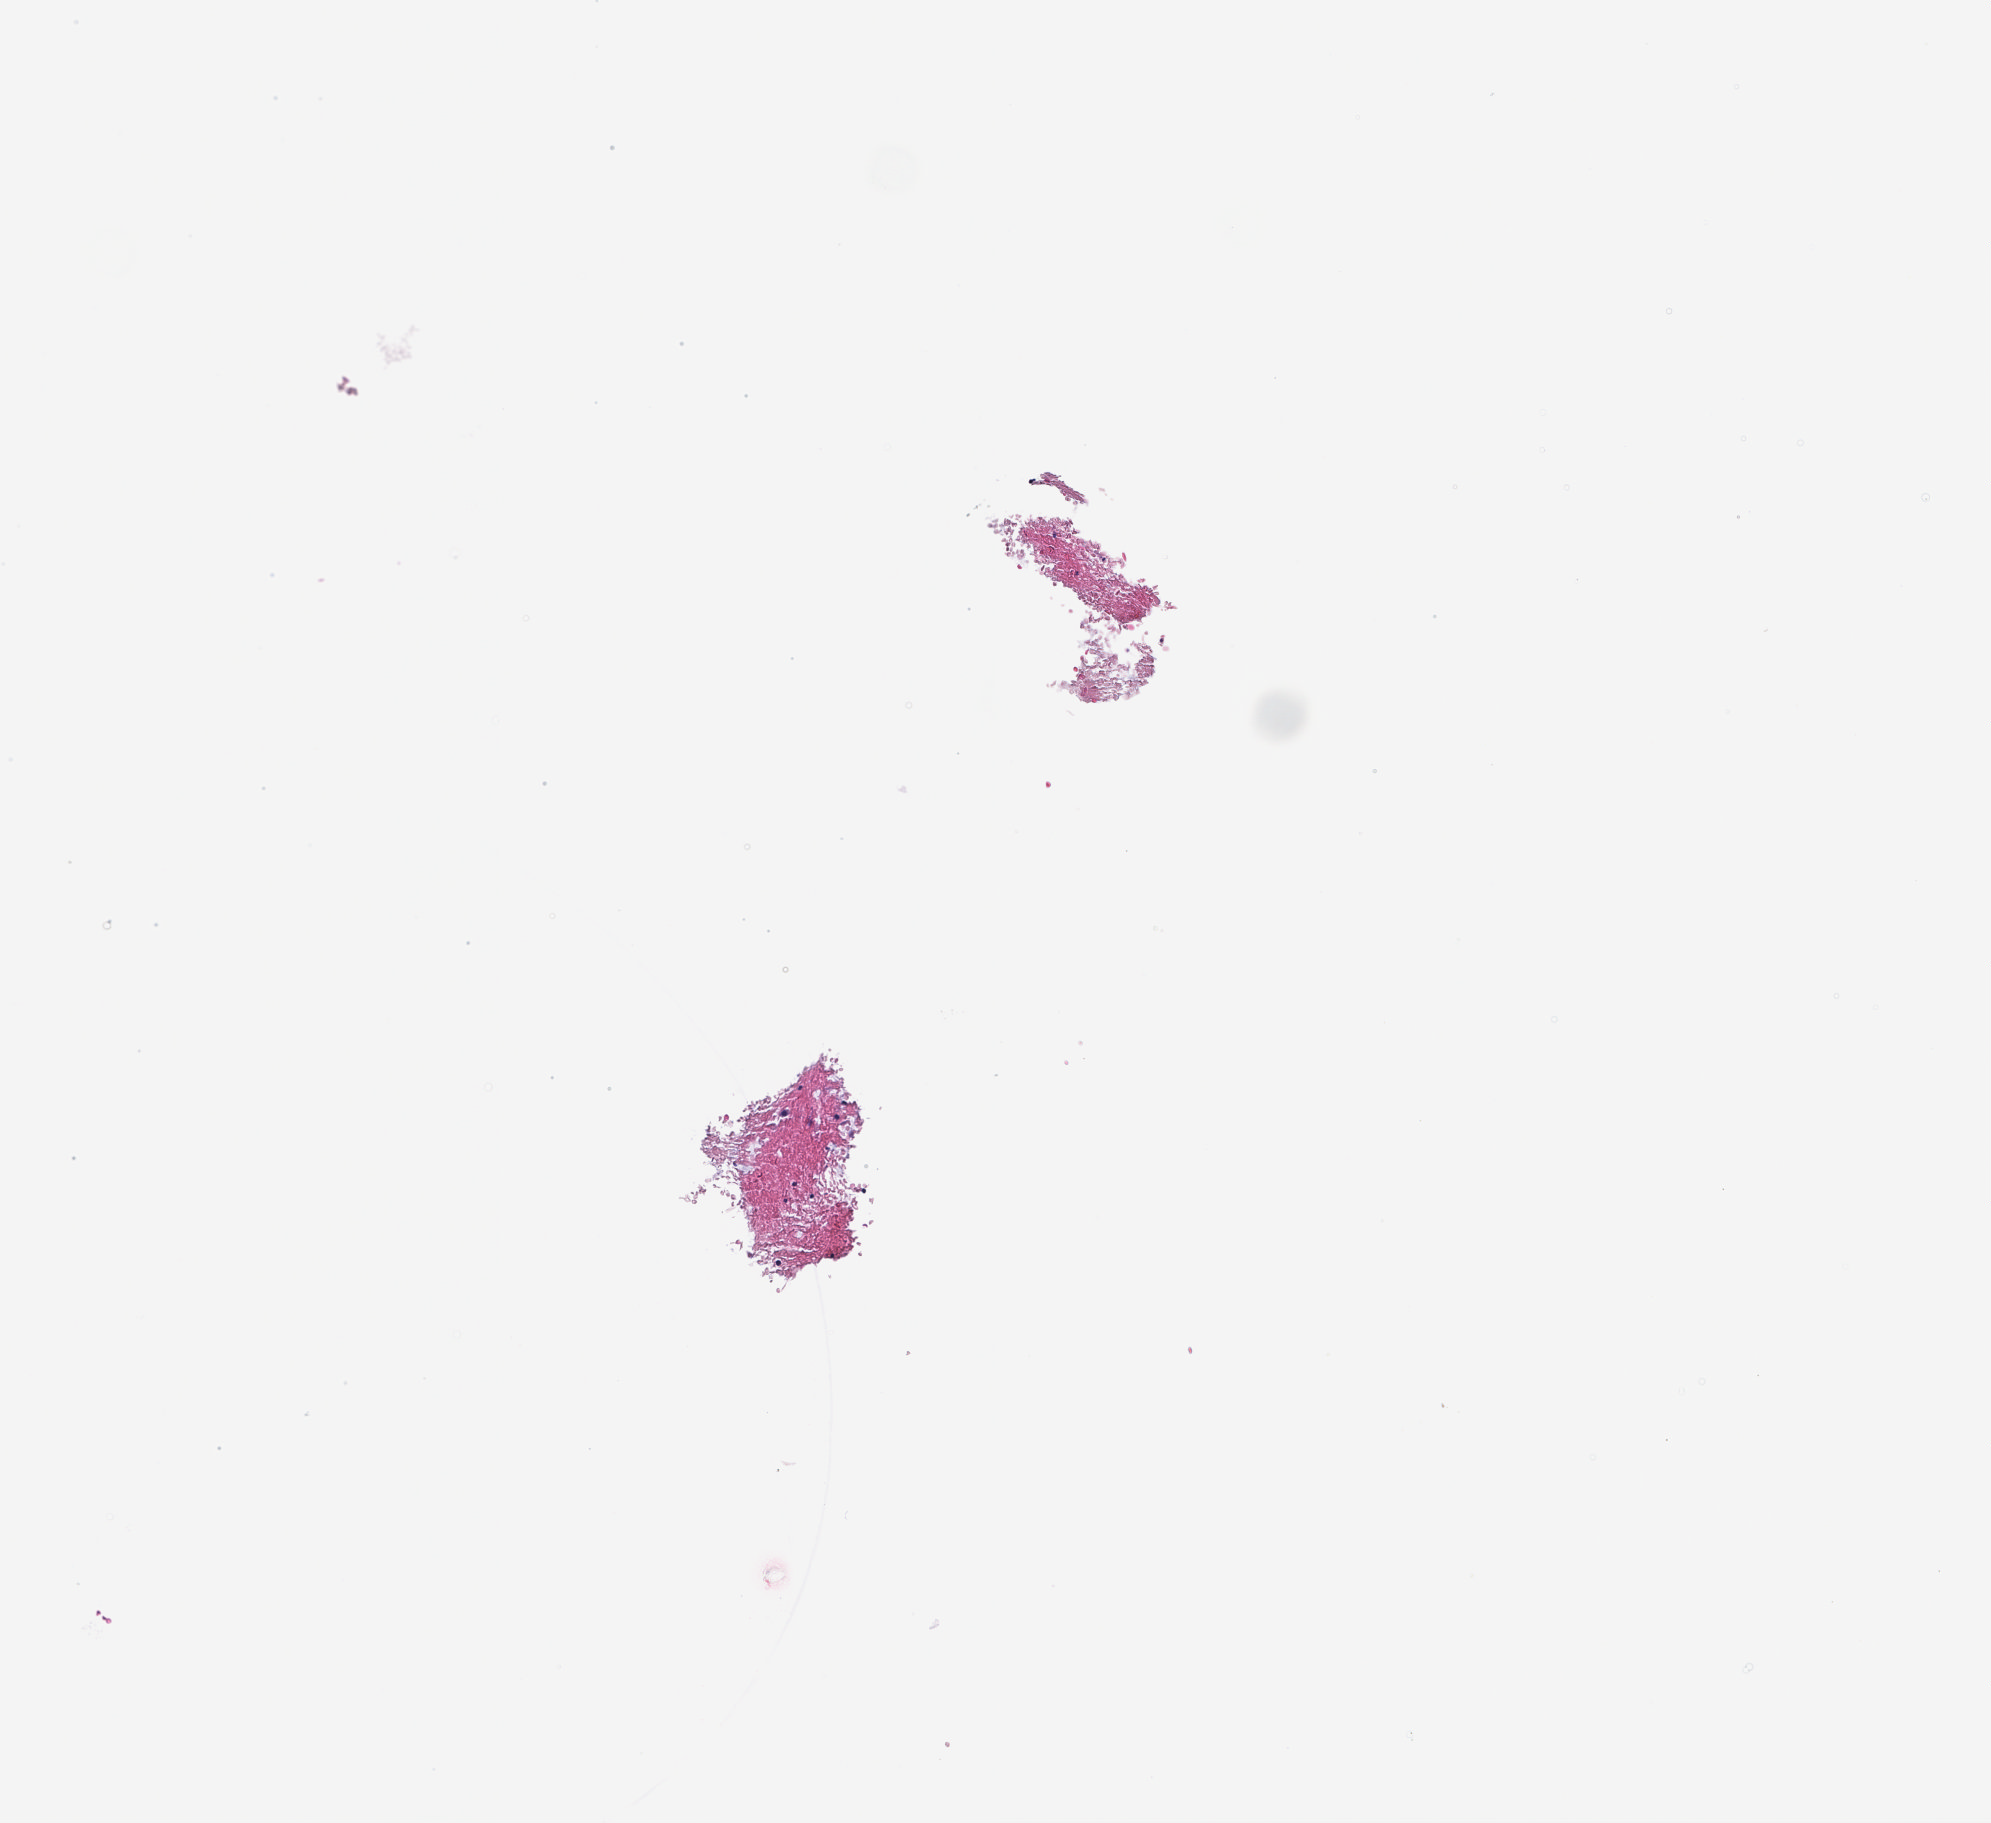
Whole-slide image, hematoxylin and eosin (H&E) stain — a low-resolution overview of the entire scanned area, about 2.0 x 1.8 mm. Formalin-fixed, paraffin-embedded (FFPE) tissue. Specimen time point: archival tissue. Patient sex: female.
This section: metastasis (sampled organ not recorded). Patient diagnosis (primary): Non-Small Cell Lung Carcinoma.